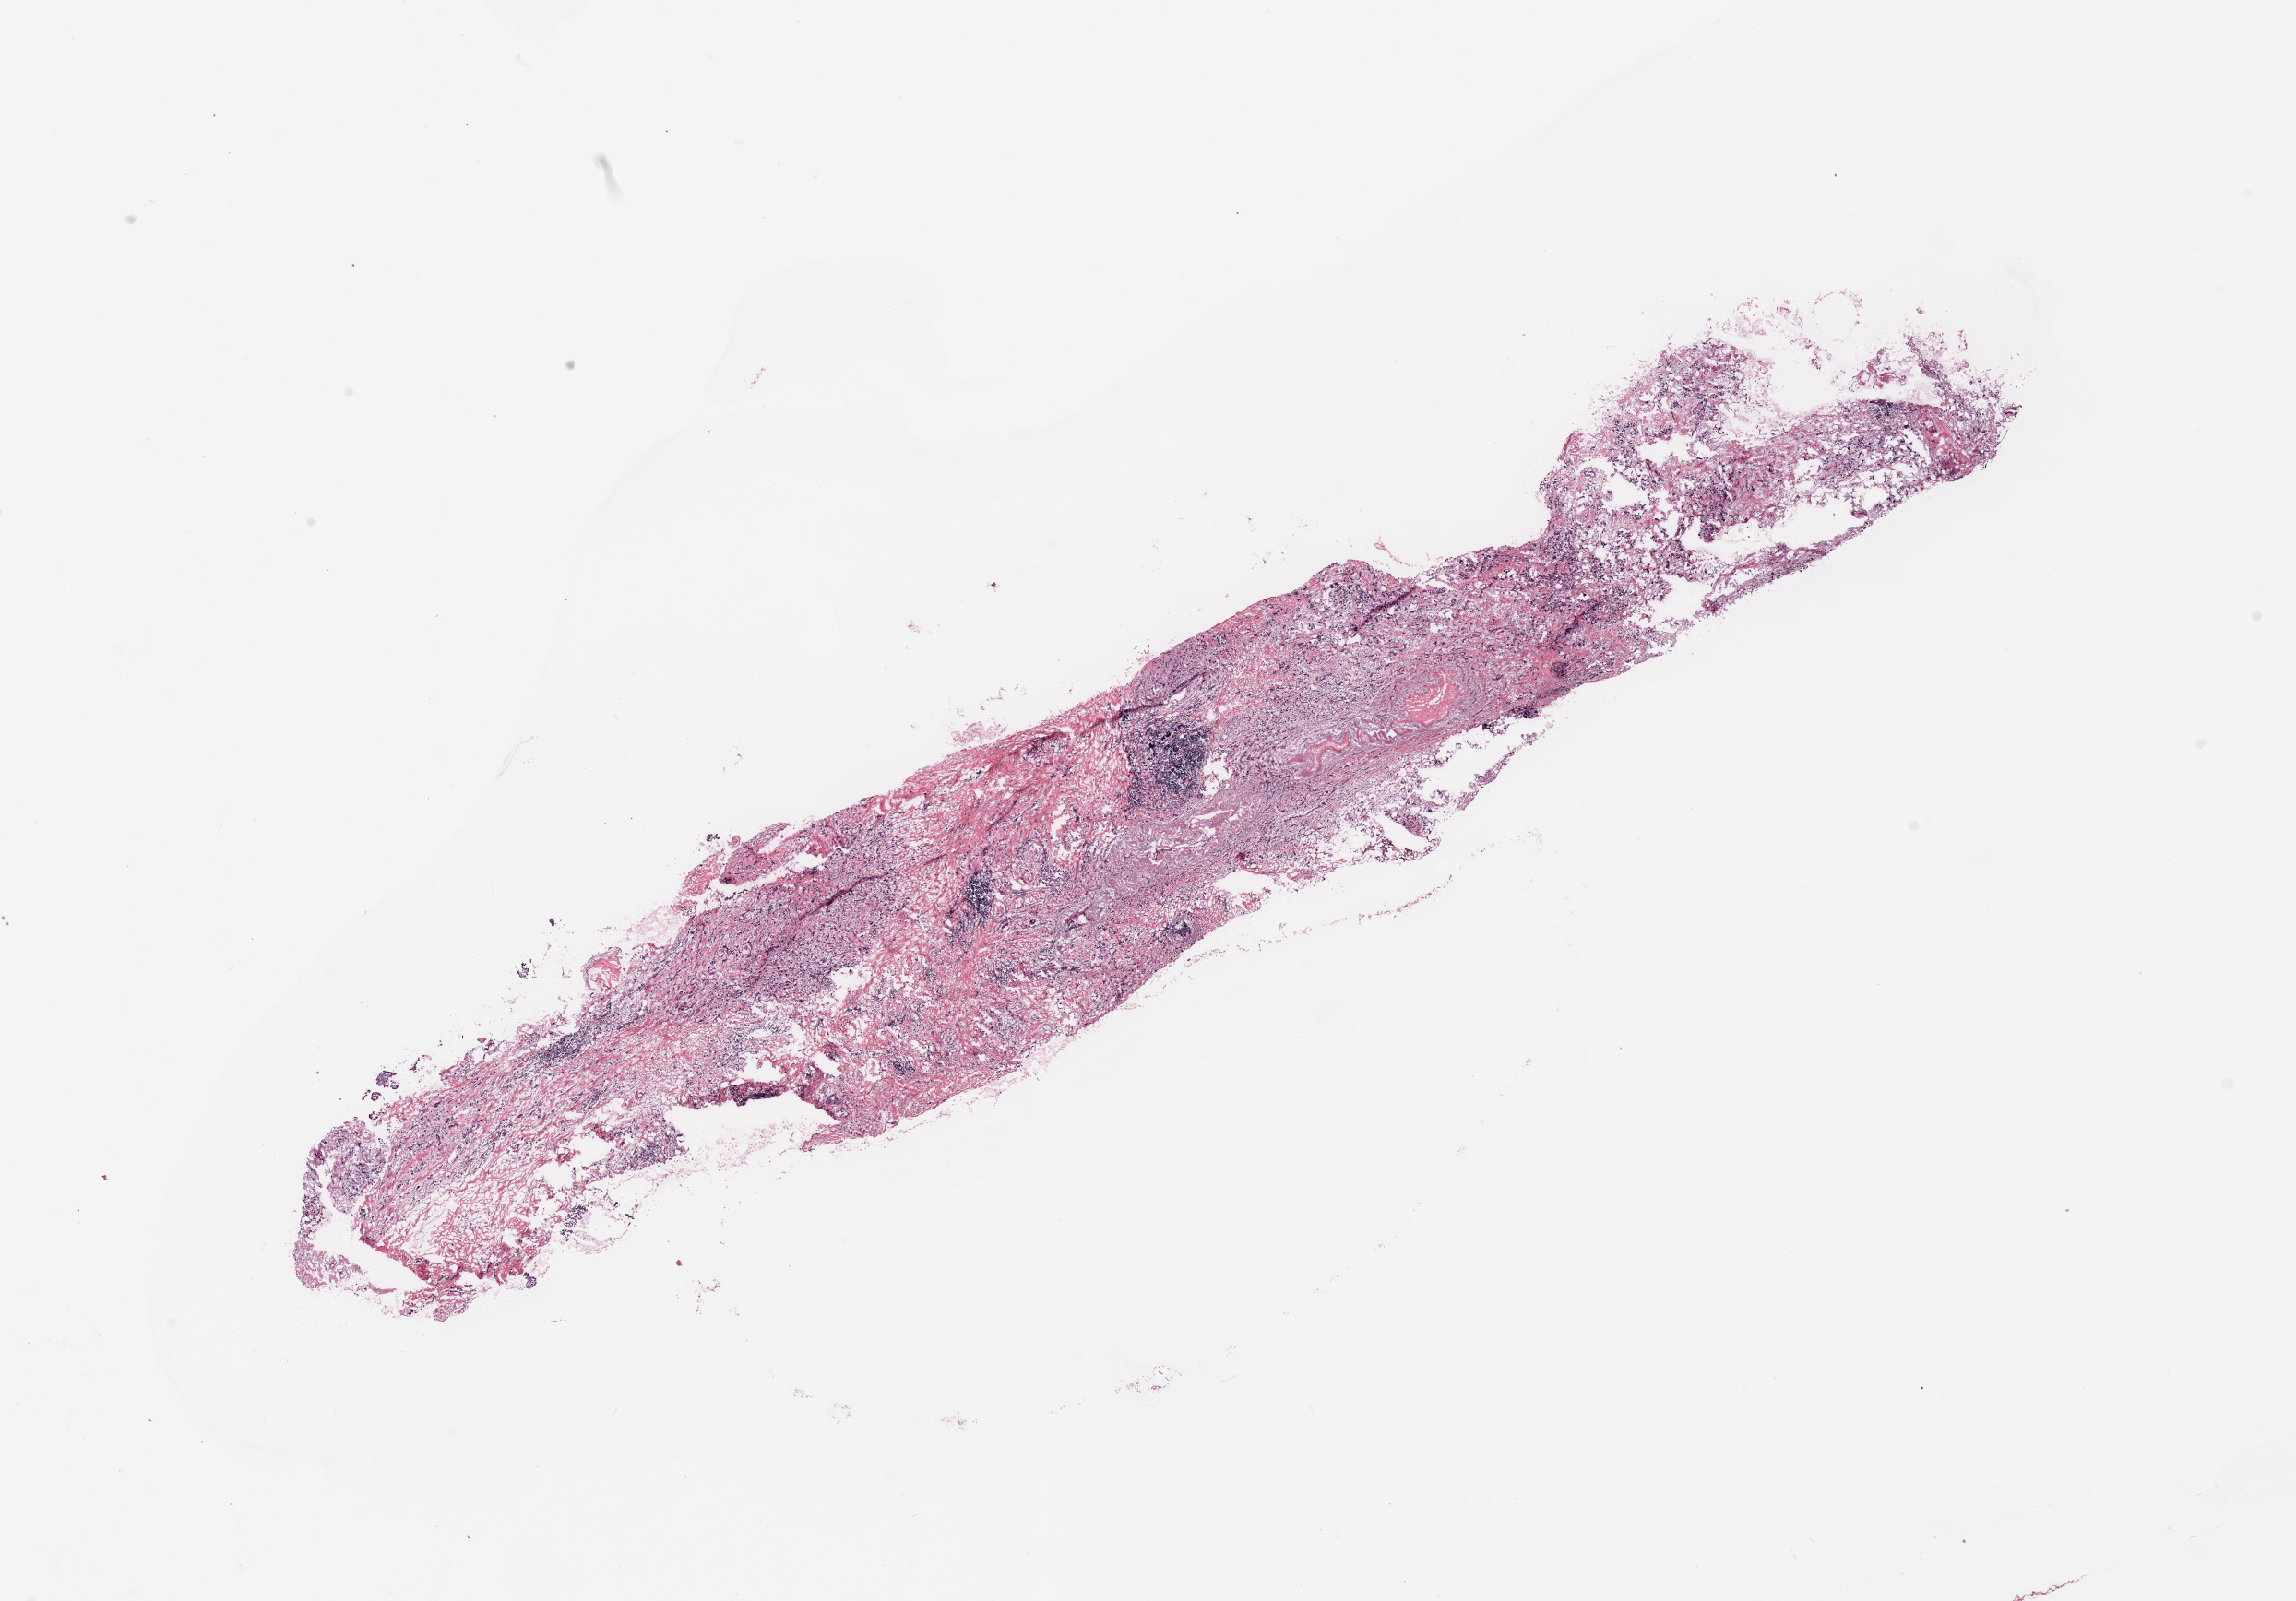
Whole-slide histology image, H&E-stained, low-resolution overview of the scanned area, about 19.7 x 13.7 mm (slide scanned at 20x), tumour tissue sample, breast. Patient: female, age 62 years.
* AJCC pathologic stage: IIIA
* histologic diagnosis: Infiltrating duct carcinoma, NOS